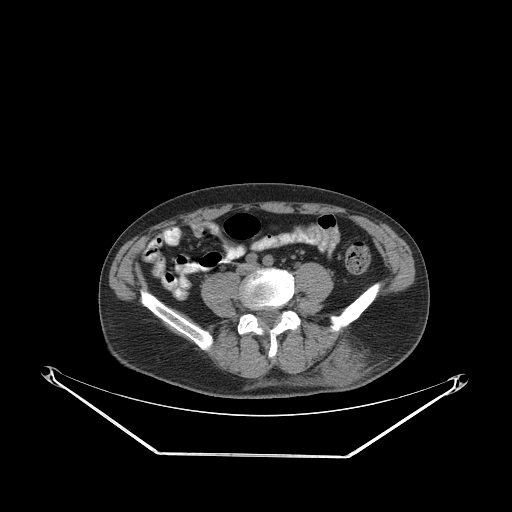
CT of an extremity soft-tissue mass (from a PET/CT study), one axial slice; position 92 of 267 along the scan axis; reconstruction kernel STANDARD; soft-tissue window (W 400 / L 40 HU); 3.75 mm slice thickness; 512 × 512 image matrix. Male patient. From the clinical record (not read from this slice): histological type: leiomyosarcoma; grade: intermediate; site of the primary tumour: left pelvis.
Annotated regions visible in this slice (expert contour drawn on MRI and transferred to this co-registered scan by the dataset authors):
- gross tumour volume (mass): bounding box [x1, y1, x2, y2] px = [322, 340, 371, 385]